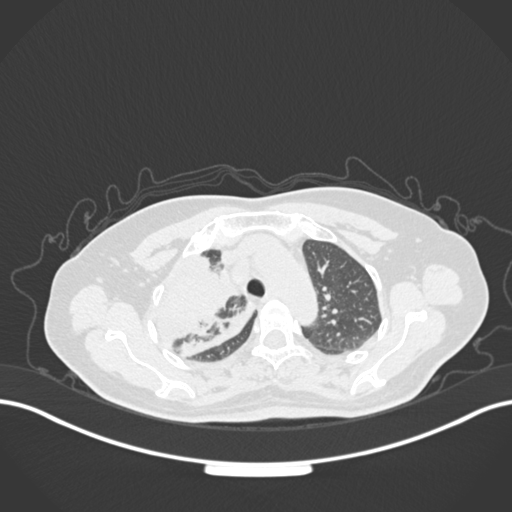
Chest CT, one axial slice; lung window (W 1500 / L -600 HU); 1 mm slice thickness; 512 × 512 image matrix, field of view 400 × 400 mm. Patient: female, 60 years. Case-level facts recorded for this patient, not image findings: clinical TNM (as recorded): T3 N1 M1.
Outlined on this slice (bounding box drawn by a radiologist):
- lung tumour (recorded histology: adenocarcinoma): bounding box <149,250,244,353> (left, top, right, bottom; pixels)